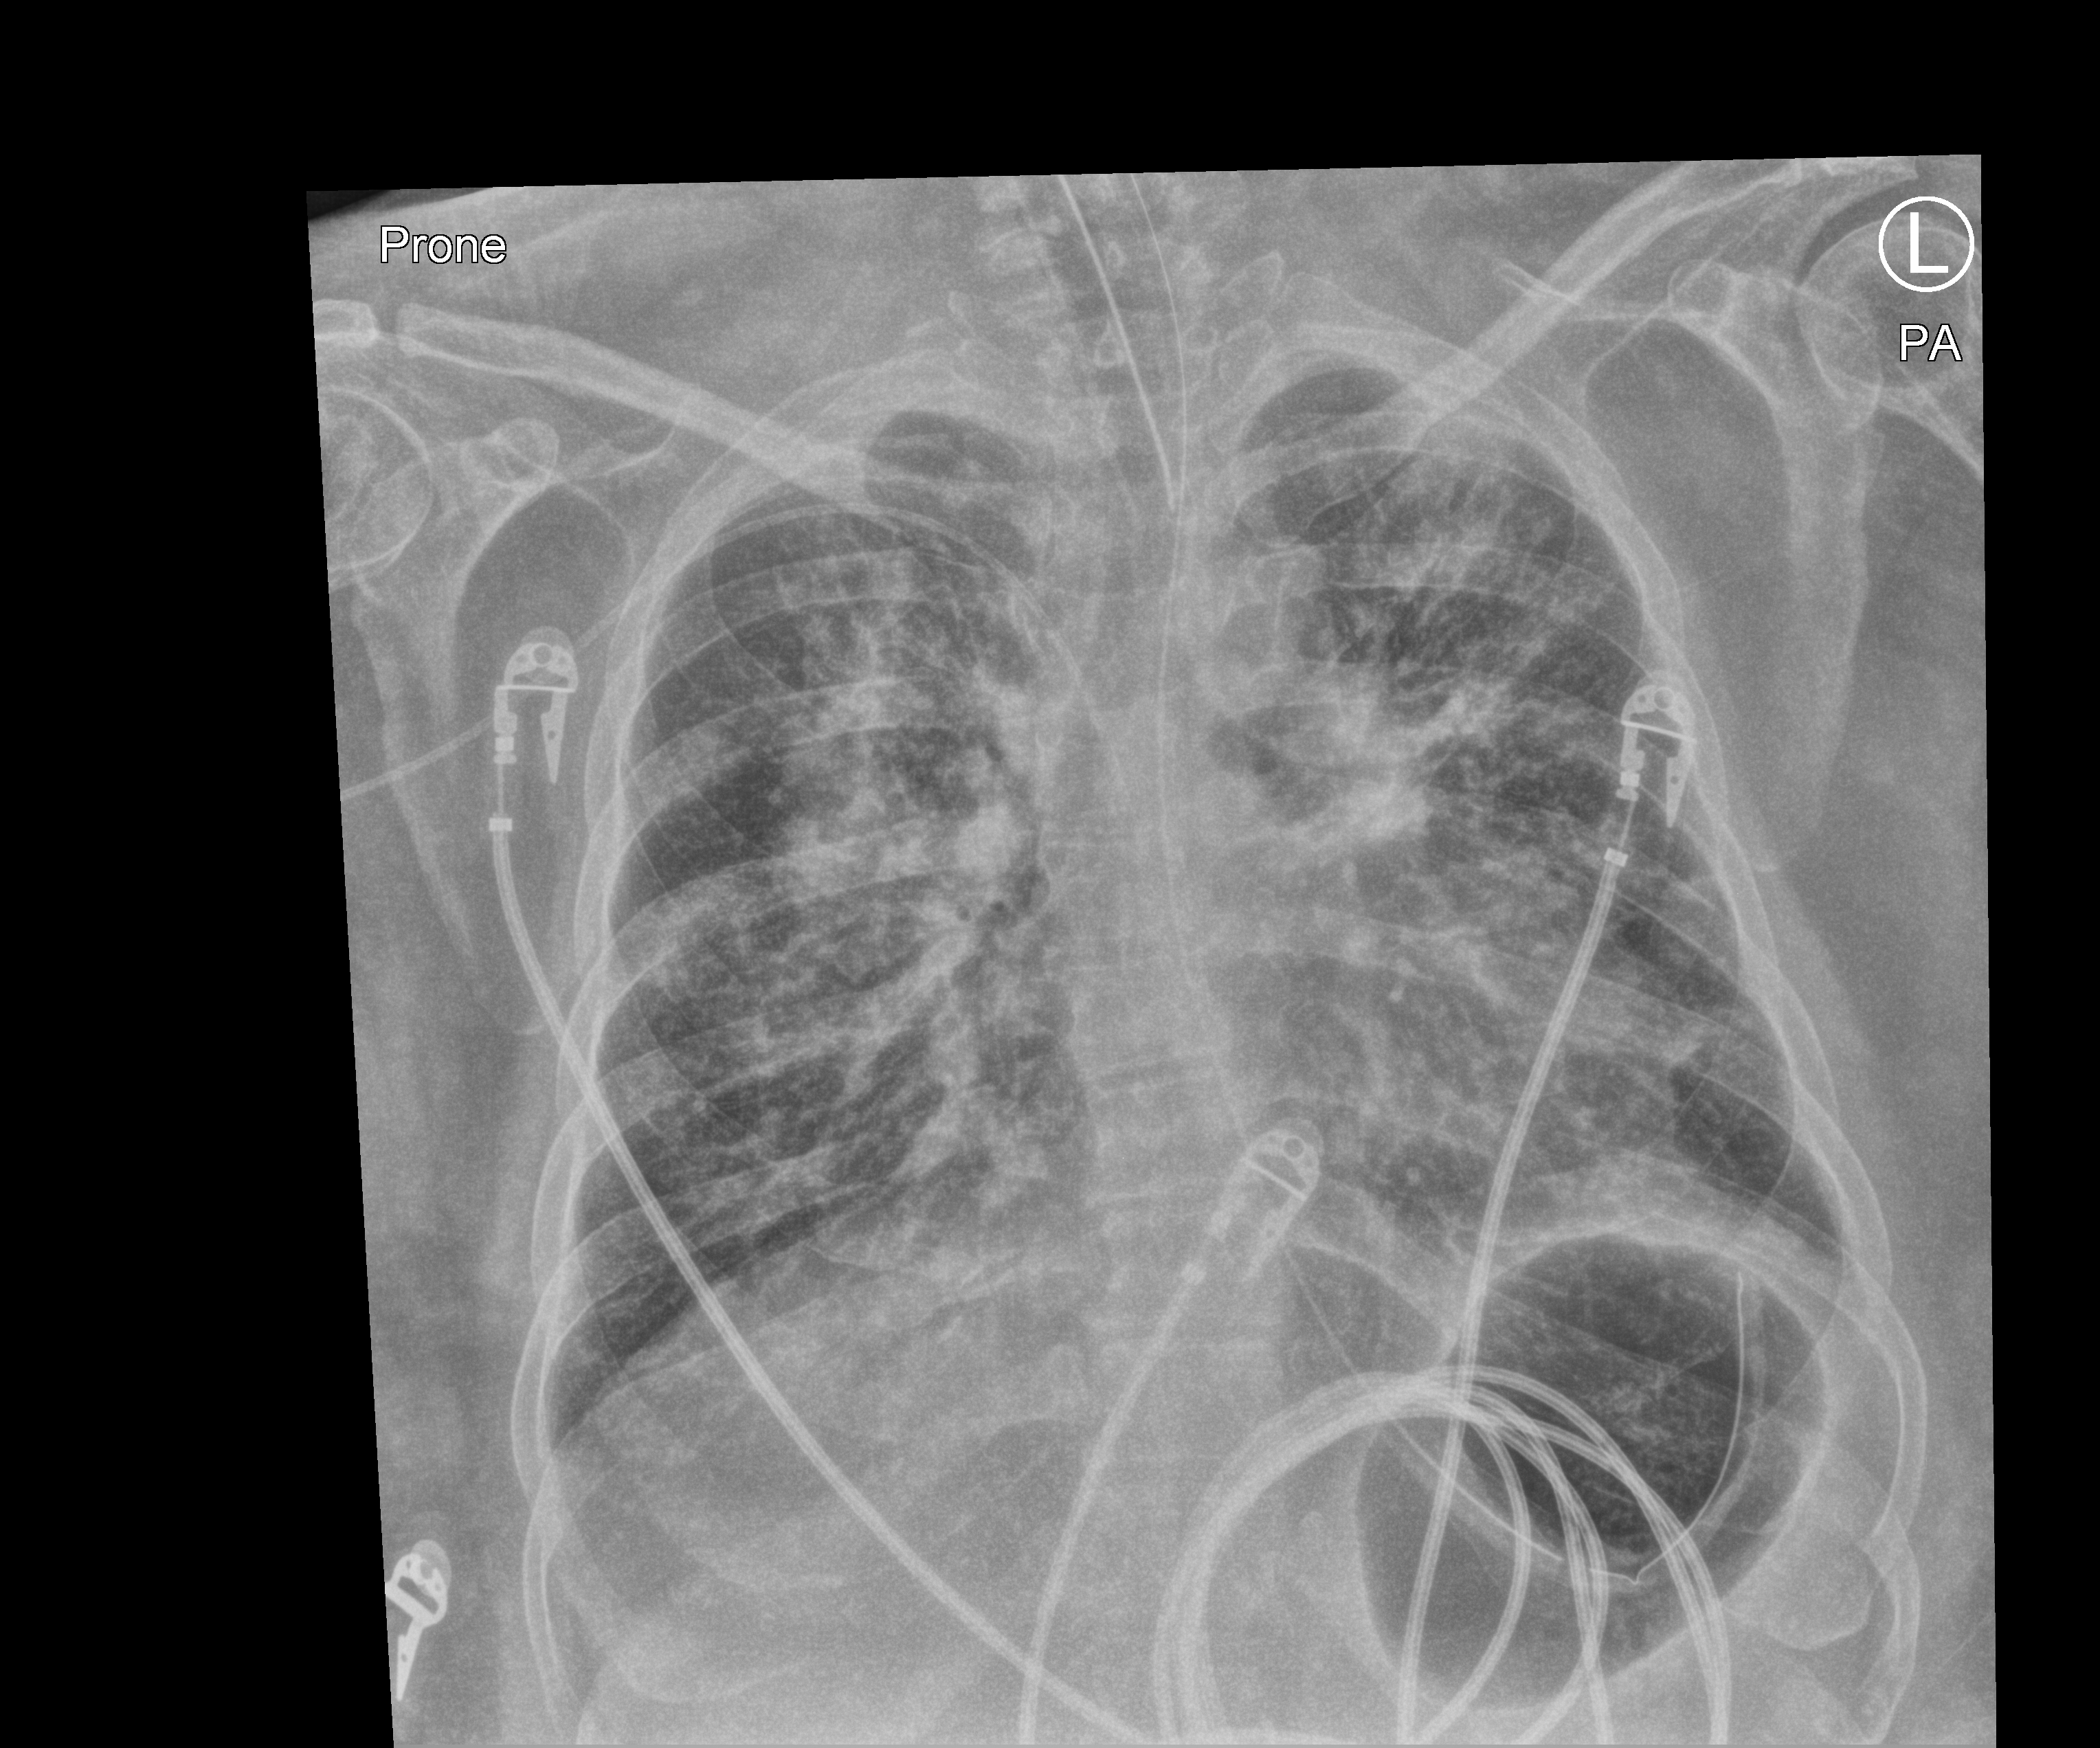
Chest X-ray (portable). Adult patient hospitalised with COVID-19, age 18–59 years.
Hospital-stay facts (about this admission, not read from this image; timing relative to this image not recorded): mechanically ventilated during this hospital stay: yes.